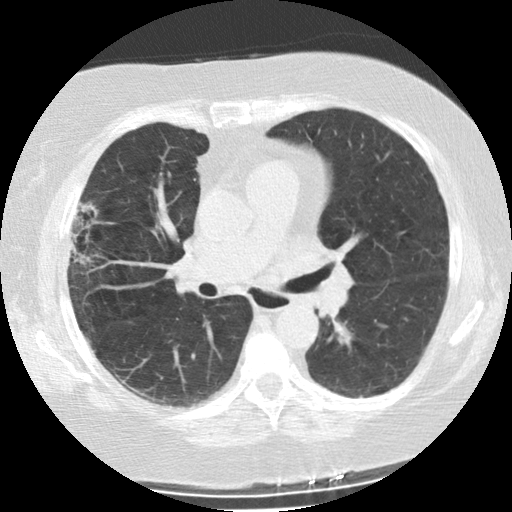
Low-dose screening chest CT, axial slice. Second screening round (one year after baseline). Lung window (W 1500 / L -600 HU). Standard (soft-tissue) reconstruction kernel (STANDARD). Slice 95 of 225 in the series. 512 × 512 image matrix. Female, age 73 years at enrolment.
Expert reader's lesion annotation, bounding box <57,199,105,275> (left, top, right, bottom; pixels). The screening reader recorded 2 non-calcified nodules or masses ≥4 mm on this exam; which of them this box marks is not recorded. Official screen result: positive, change unspecified: nodule(s) >= 4 mm or enlarging nodule(s), mass(es), or other non-specific abnormalities suspicious for lung cancer. Participant outcome: lung cancer diagnosed 47 days after this screen — bronchiolo-alveolar adenocarcinoma, NOS, right upper lobe, moderately differentiated (G2), stage IIIB (AJCC 6th edition), 21 mm at pathology.